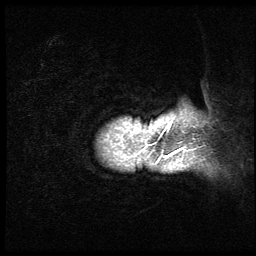
Breast MRI (dynamic contrast-enhanced), one sagittal slice; position 4 of 64 along the scan axis; 3 images stored at this slice position (order not interpretable as contrast timing); 1.5 T; TE 4.2 ms, TR 9 ms; 256 × 256 image matrix, field of view 180 × 180 mm. Patient: female, 50 years. Case-level facts recorded for this patient, not image findings: setting: breast cancer imaged before/during neoadjuvant chemotherapy; receptor status: triple-negative.
Annotated regions visible in this slice (semi-automatically segmented with operator editing):
- analysis volume of interest (the breast-tissue region the enhancement analysis was run in; not a lesion): bounding box (x1, y1, x2, y2) in pixels: (82, 86, 194, 209)
- tumour enhancement mask (voxels above the 140 % enhancement threshold inside the analysis volume of interest): (97, 116, 186, 165)